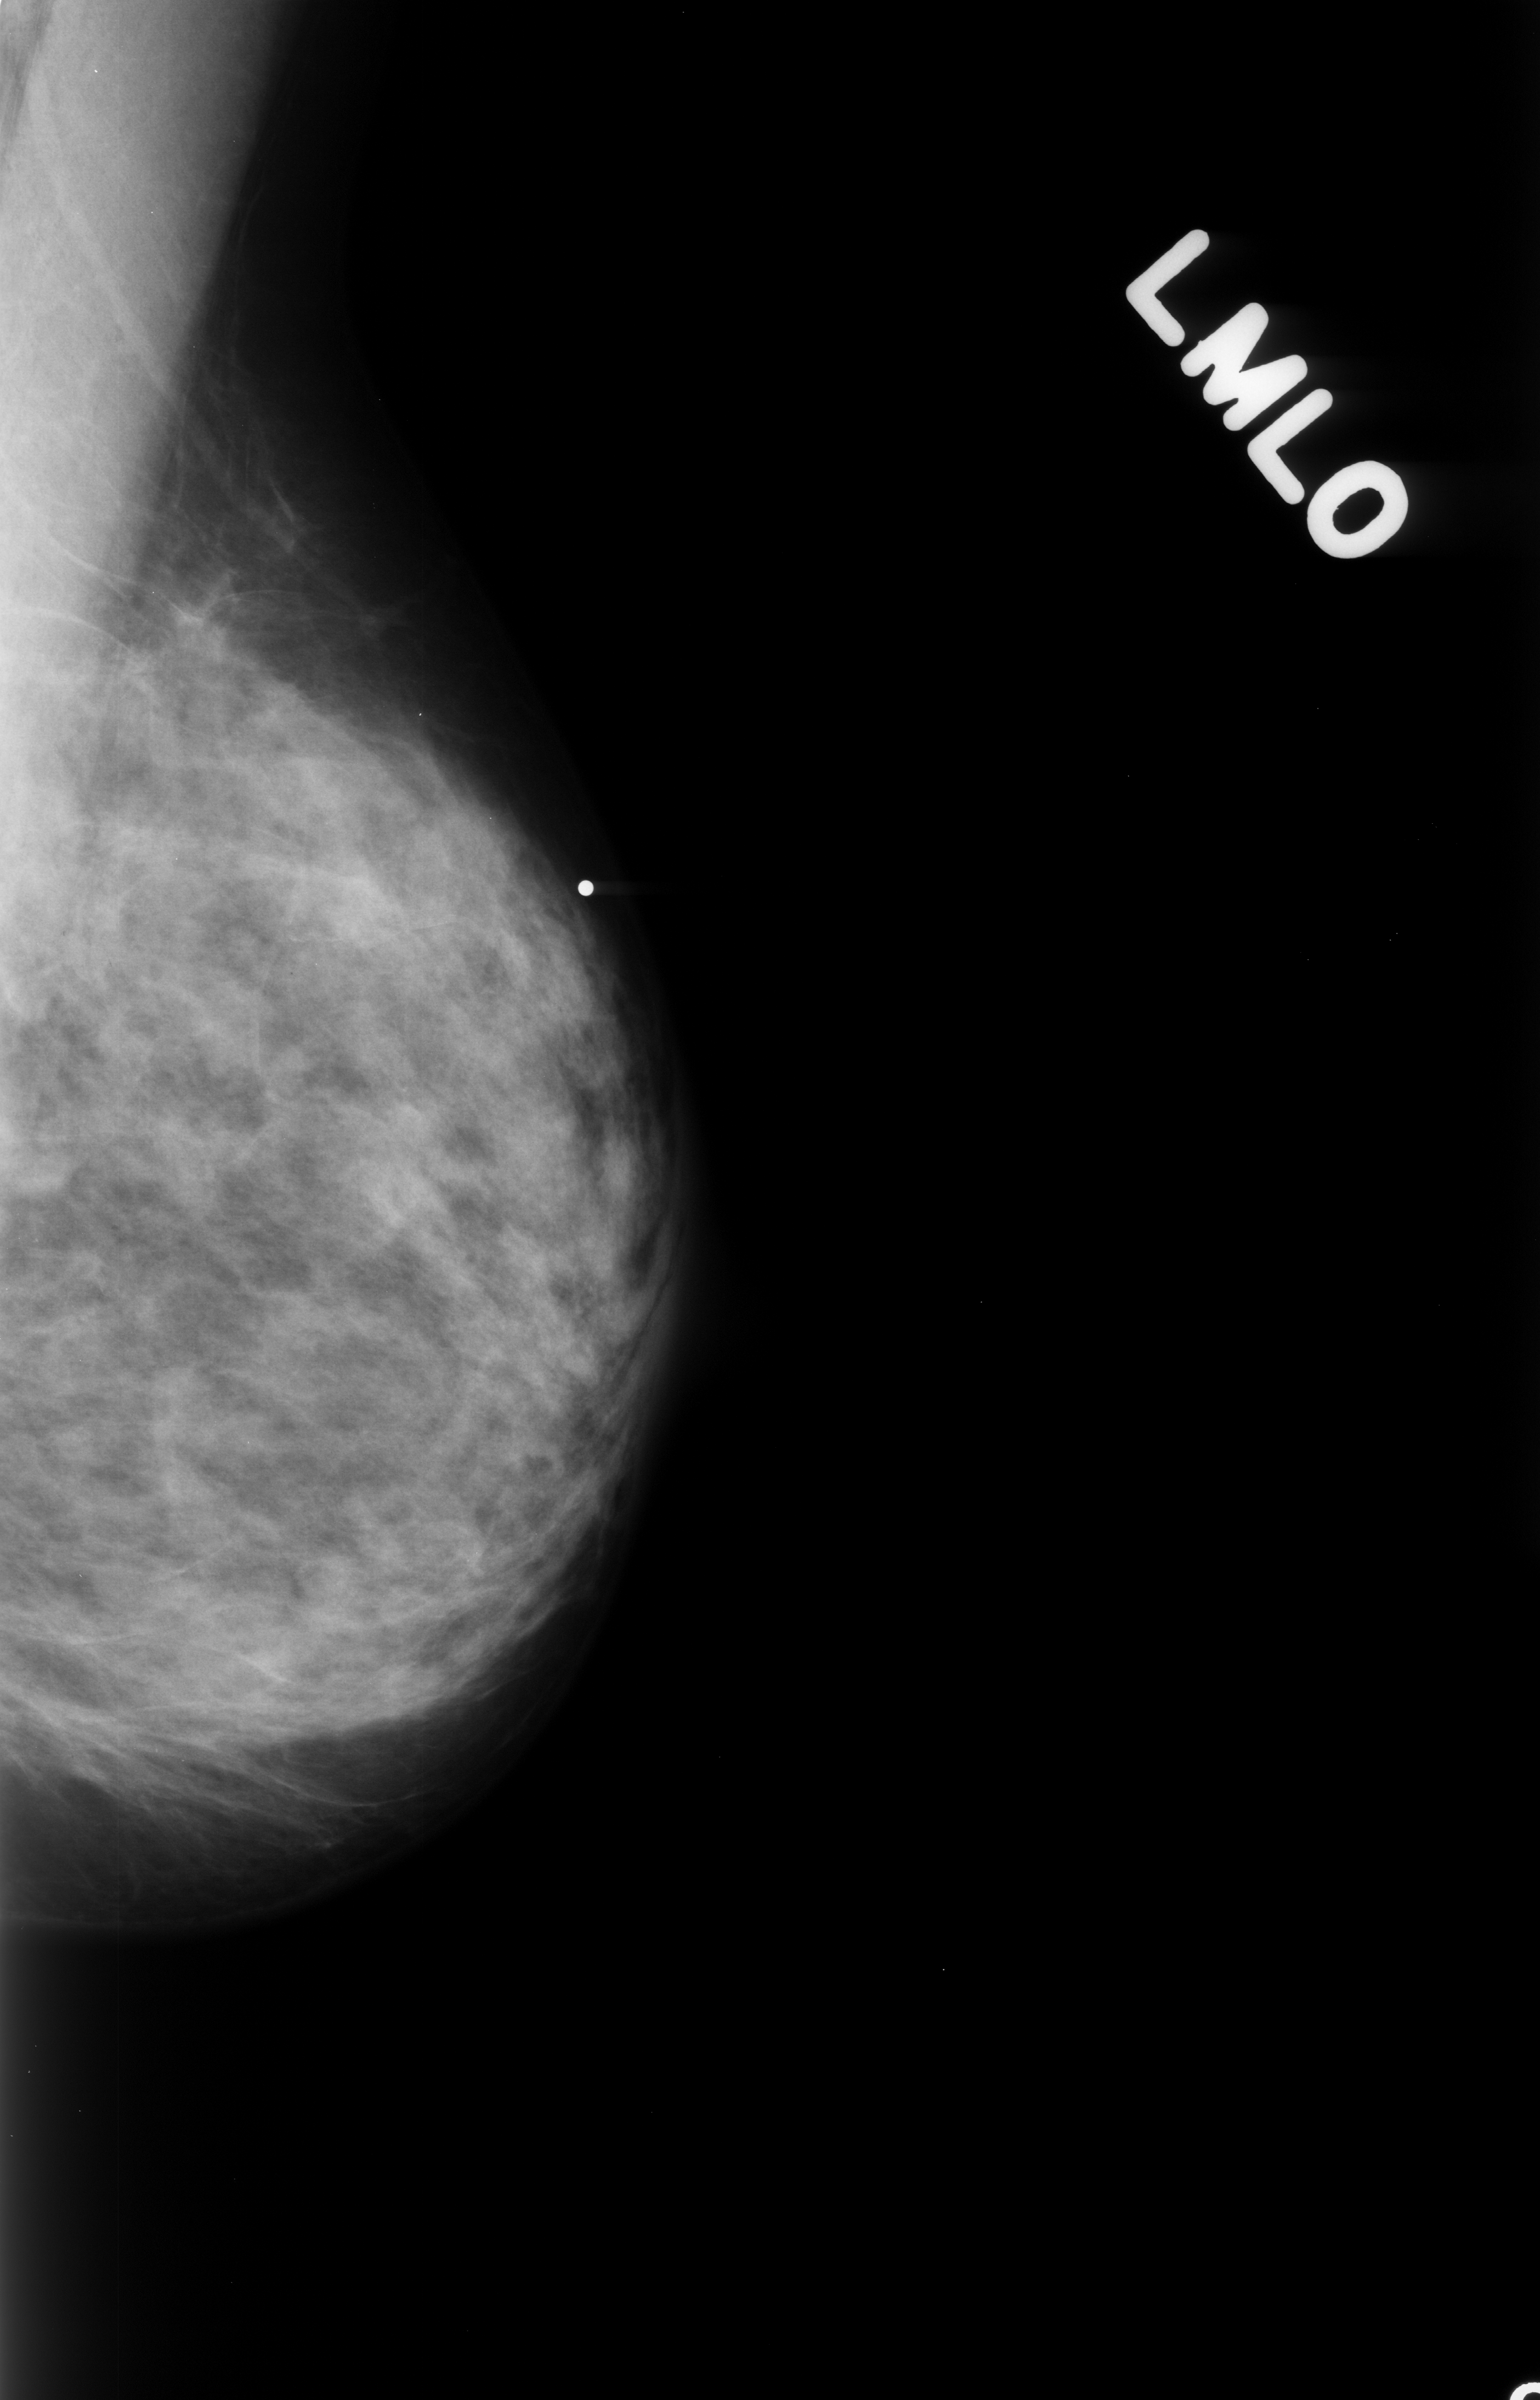
Scanned film-screen mammogram; left breast; MLO view; breast composition: heterogeneously dense (BI-RADS density category 3 of 4); 1540 × 2400 image matrix.
Expert-marked regions of interest on this film, with their recorded descriptors:
- mass, shape focal asymmetric density, margins ill defined; BI-RADS assessment category 3; subtlety rating 1 on a 1 (subtle) to 5 (obvious) scale; pathology (as recorded): benign: box from (x=0, y=751) to (x=110, y=924) px